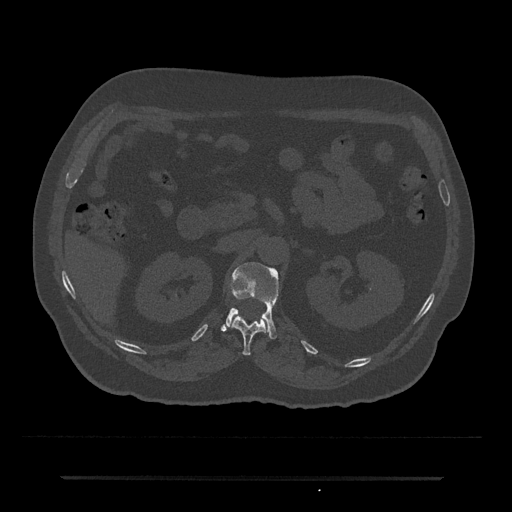
CT including the spine, one axial slice. Slice 100 of 797 in the series (ordered by position). Bone window (W 1800 / L 400 HU). 0.5 mm slice thickness. 512 × 512 image matrix, field of view 437 × 437 mm. Patient: male, 69 years. Case-level facts recorded for this patient, not image findings: primary cancer: prostate.
Outlined on this slice (semi-automatic segmentation, software-assisted and operator-edited):
- L1 vertebra: bounding box <222,262,279,339> (left, top, right, bottom; pixels)
- T12 vertebra: <231,313,269,355>